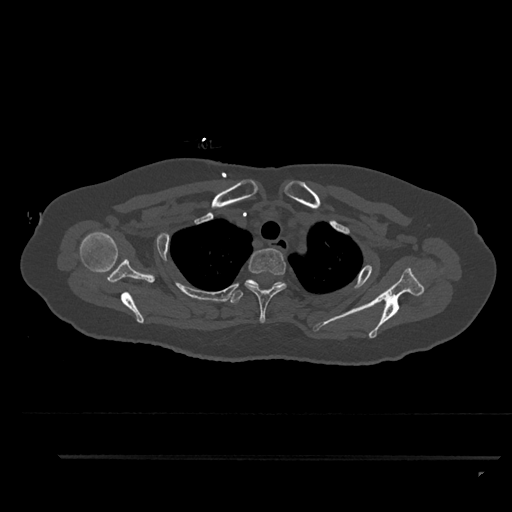
CT including the spine, one axial slice. Position 711 of 797 along the scan axis. Reconstruction kernel Br40s/3. 120 kVp. Bone window (W 1800 / L 400 HU). 512 × 512 image matrix, field of view 408 × 408 mm. Female patient, age 44 years. From the clinical record (not read from this slice): primary cancer: renal; vertebrae with lytic lesions (as recorded): L1.
Outlined on this slice (semi-automatic segmentation, software-assisted and operator-edited):
- T1 vertebra: bounding box <272,283,285,288> (left, top, right, bottom; pixels)
- T2 vertebra: <245,248,287,323>
- T3 vertebra: <230,279,283,304>